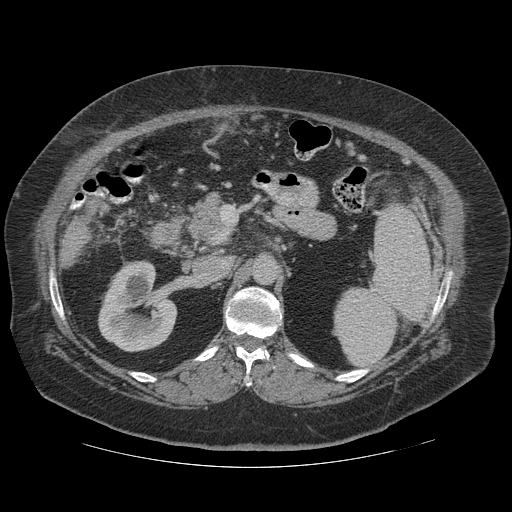
Contrast-enhanced abdominal CT (liver protocol), one axial slice. Slice 55 of 121 in the series (ordered by position). Soft-tissue window (W 400 / L 40 HU). 2.5 mm slice thickness. 512 × 512 image matrix, field of view 420 × 420 mm. Case-level facts recorded for this patient, not image findings: diagnosis: hepatocellular carcinoma (patient treated with transarterial chemoembolisation; whether this scan precedes or follows treatment is not stated here); TNM stage (as recorded): Stage-IIIA; Child-Pugh class: A; tumour differentiation: well differentiated; tumour nodularity: multinodular.
Outlined on this slice (semi-automatic segmentation, software-assisted and operator-edited):
- liver parenchyma outside the tumour (the mass and vessels are separate outlines, so this box may not span the whole liver): box from (x=60, y=220) to (x=88, y=266) px